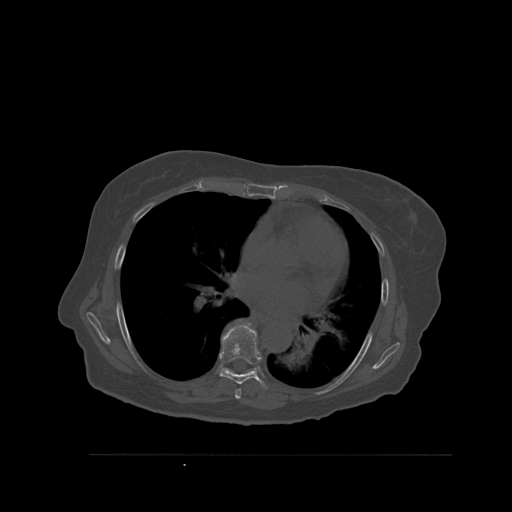
CT including the spine, one axial slice; slice 364 of 527 in the series (ordered by position); bone window (W 1800 / L 400 HU); 512 × 512 image matrix, field of view 470 × 470 mm. Female patient, age 73 years. From the clinical record (not read from this slice): primary cancer: breast; vertebrae with lytic lesions (as recorded): L2.
Annotated regions visible in this slice (semi-automatically segmented with operator editing):
- T6 vertebra: box from (x=235, y=389) to (x=241, y=399) px
- T7 vertebra: (x=219, y=323)–(x=265, y=388)
- T8 vertebra: (x=227, y=319)–(x=254, y=372)